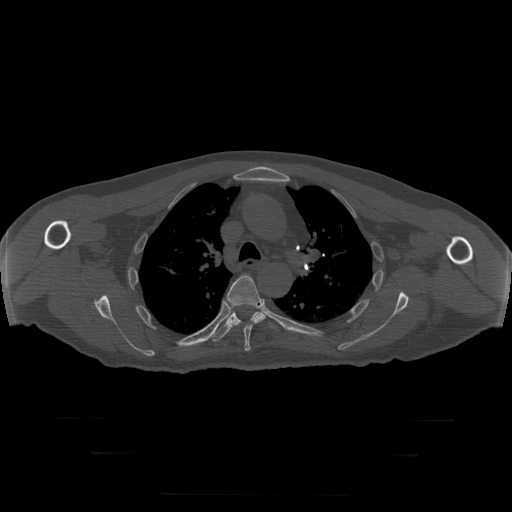
CT including the spine, one axial slice. Reconstruction kernel STANDARD. Bone window (W 1800 / L 400 HU). 1.25 mm slice thickness. 512 × 512 image matrix, field of view 510 × 510 mm. Patient age 73 years. Case-level facts recorded for this patient, not image findings: primary cancer: prostate.
Structures marked on this image (semi-automatic segmentation, software-assisted and operator-edited):
- T5 vertebra: bounding box (x1, y1, x2, y2) in pixels: (227, 276, 266, 352)
- T6 vertebra: (209, 311, 272, 342)